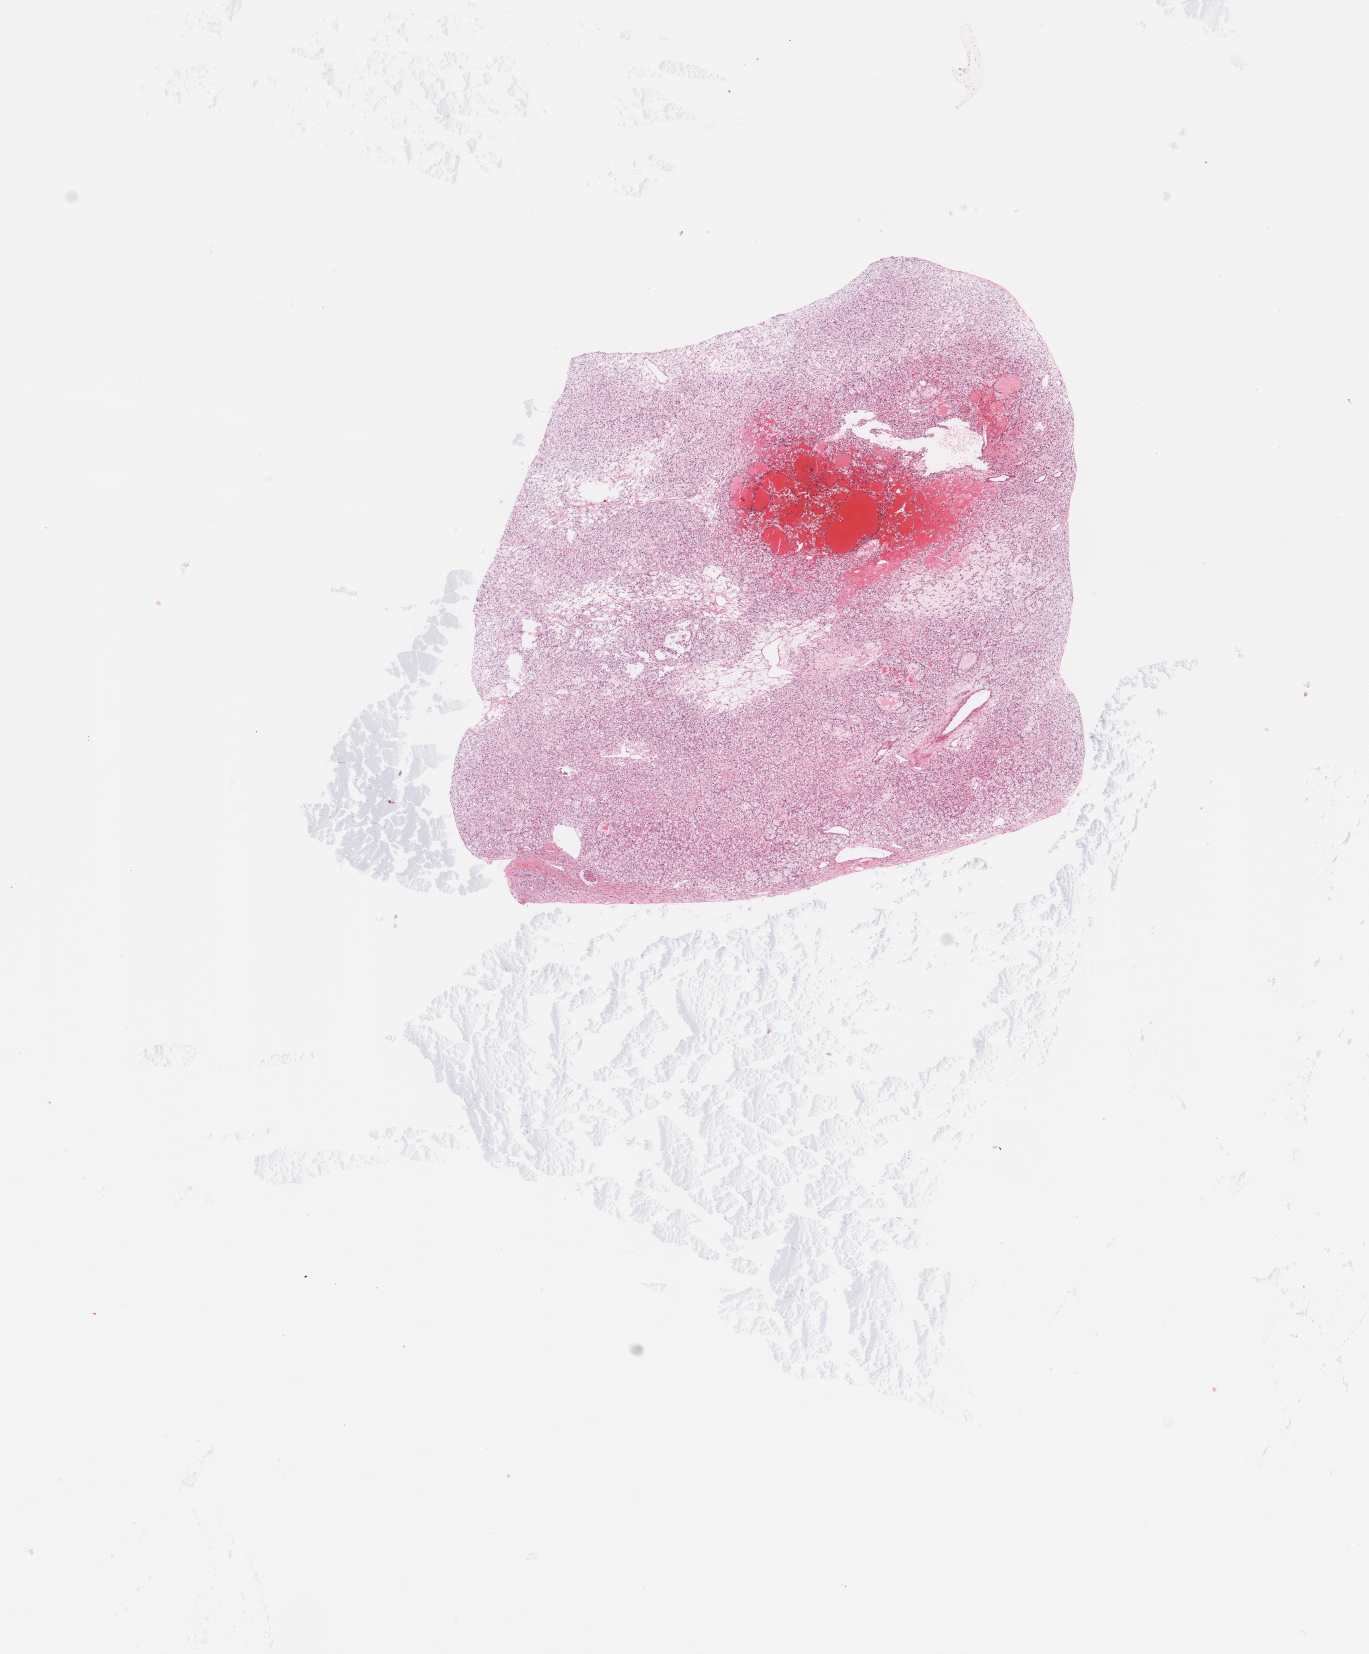
Digitized Hematoxylin and eosin (H&E) stained tissue section (whole slide), a low-resolution overview of the entire scanned area, about 10.8 x 13.1 mm. Tumour tissue sample, sampled site: kidney. Female, 47 y/o. Histologic grade: G2 (moderately differentiated). Slide review estimates, as recorded: tumour nuclei 85%, necrosis 3%.
Diagnosis: Renal cell carcinoma, NOS. AJCC pathologic stage: I. Primary tumour site (as recorded): lower pole.